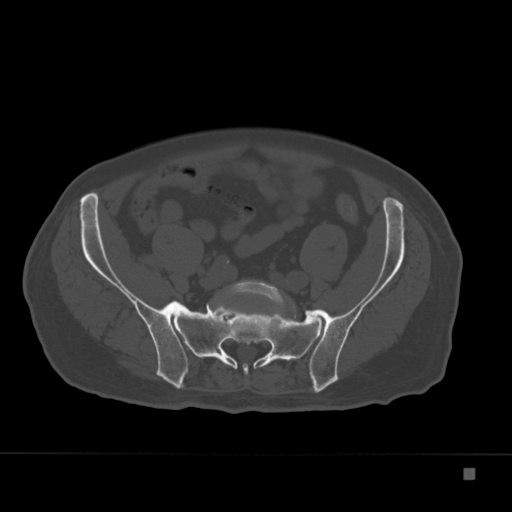
CT including the spine, one axial slice. Position 7 of 332 along the scan axis. 120 kVp. Bone window (W 1800 / L 400 HU). 512 × 512 image matrix, field of view 389 × 389 mm. Patient: male, 72 years. Case-level facts recorded for this patient, not image findings: primary cancer: skeletal.
Annotated regions visible in this slice (semi-automatic segmentation, software-assisted and operator-edited):
- L5 vertebra: box from (x=227, y=281) to (x=291, y=308) px